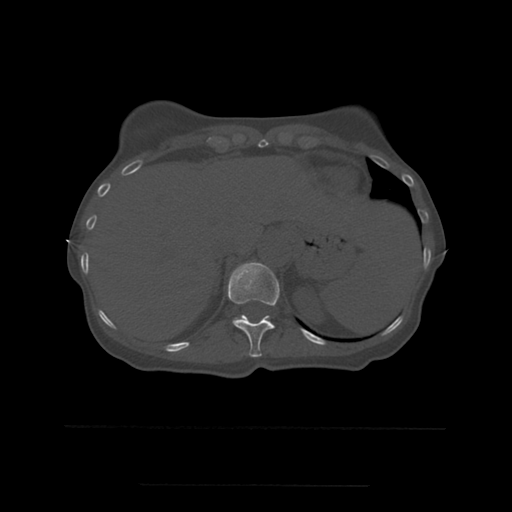
CT including the spine, one axial slice. Slice 276 of 544 in the series (ordered by position). Bone window (W 1800 / L 400 HU). 1.25 mm slice thickness. 512 × 512 image matrix, field of view 350 × 350 mm. Patient age 58 years. Case-level facts recorded for this patient, not image findings: primary cancer: lung.
Annotated regions visible in this slice (semi-automatic segmentation, software-assisted and operator-edited):
- T11 vertebra: box from (x=228, y=263) to (x=280, y=358) px
- T12 vertebra: (x=234, y=318)–(x=264, y=321)